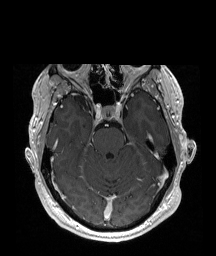
Brain MRI from a brain-tumour surgery series, one axial slice; position 129 of 192 along the scan axis; T1-weighted post-contrast; 216 × 256 image matrix, field of view 219 × 260 mm. Case-level facts recorded for this patient, not image findings: histopathology: Astrocytoma; WHO grade: 2; IDH mutation: yes; tumour location: Right Insular.
Annotated regions visible in this slice (expert manual segmentation):
- tumour: bounding box (x1, y1, x2, y2) in pixels: (74, 96, 88, 110)